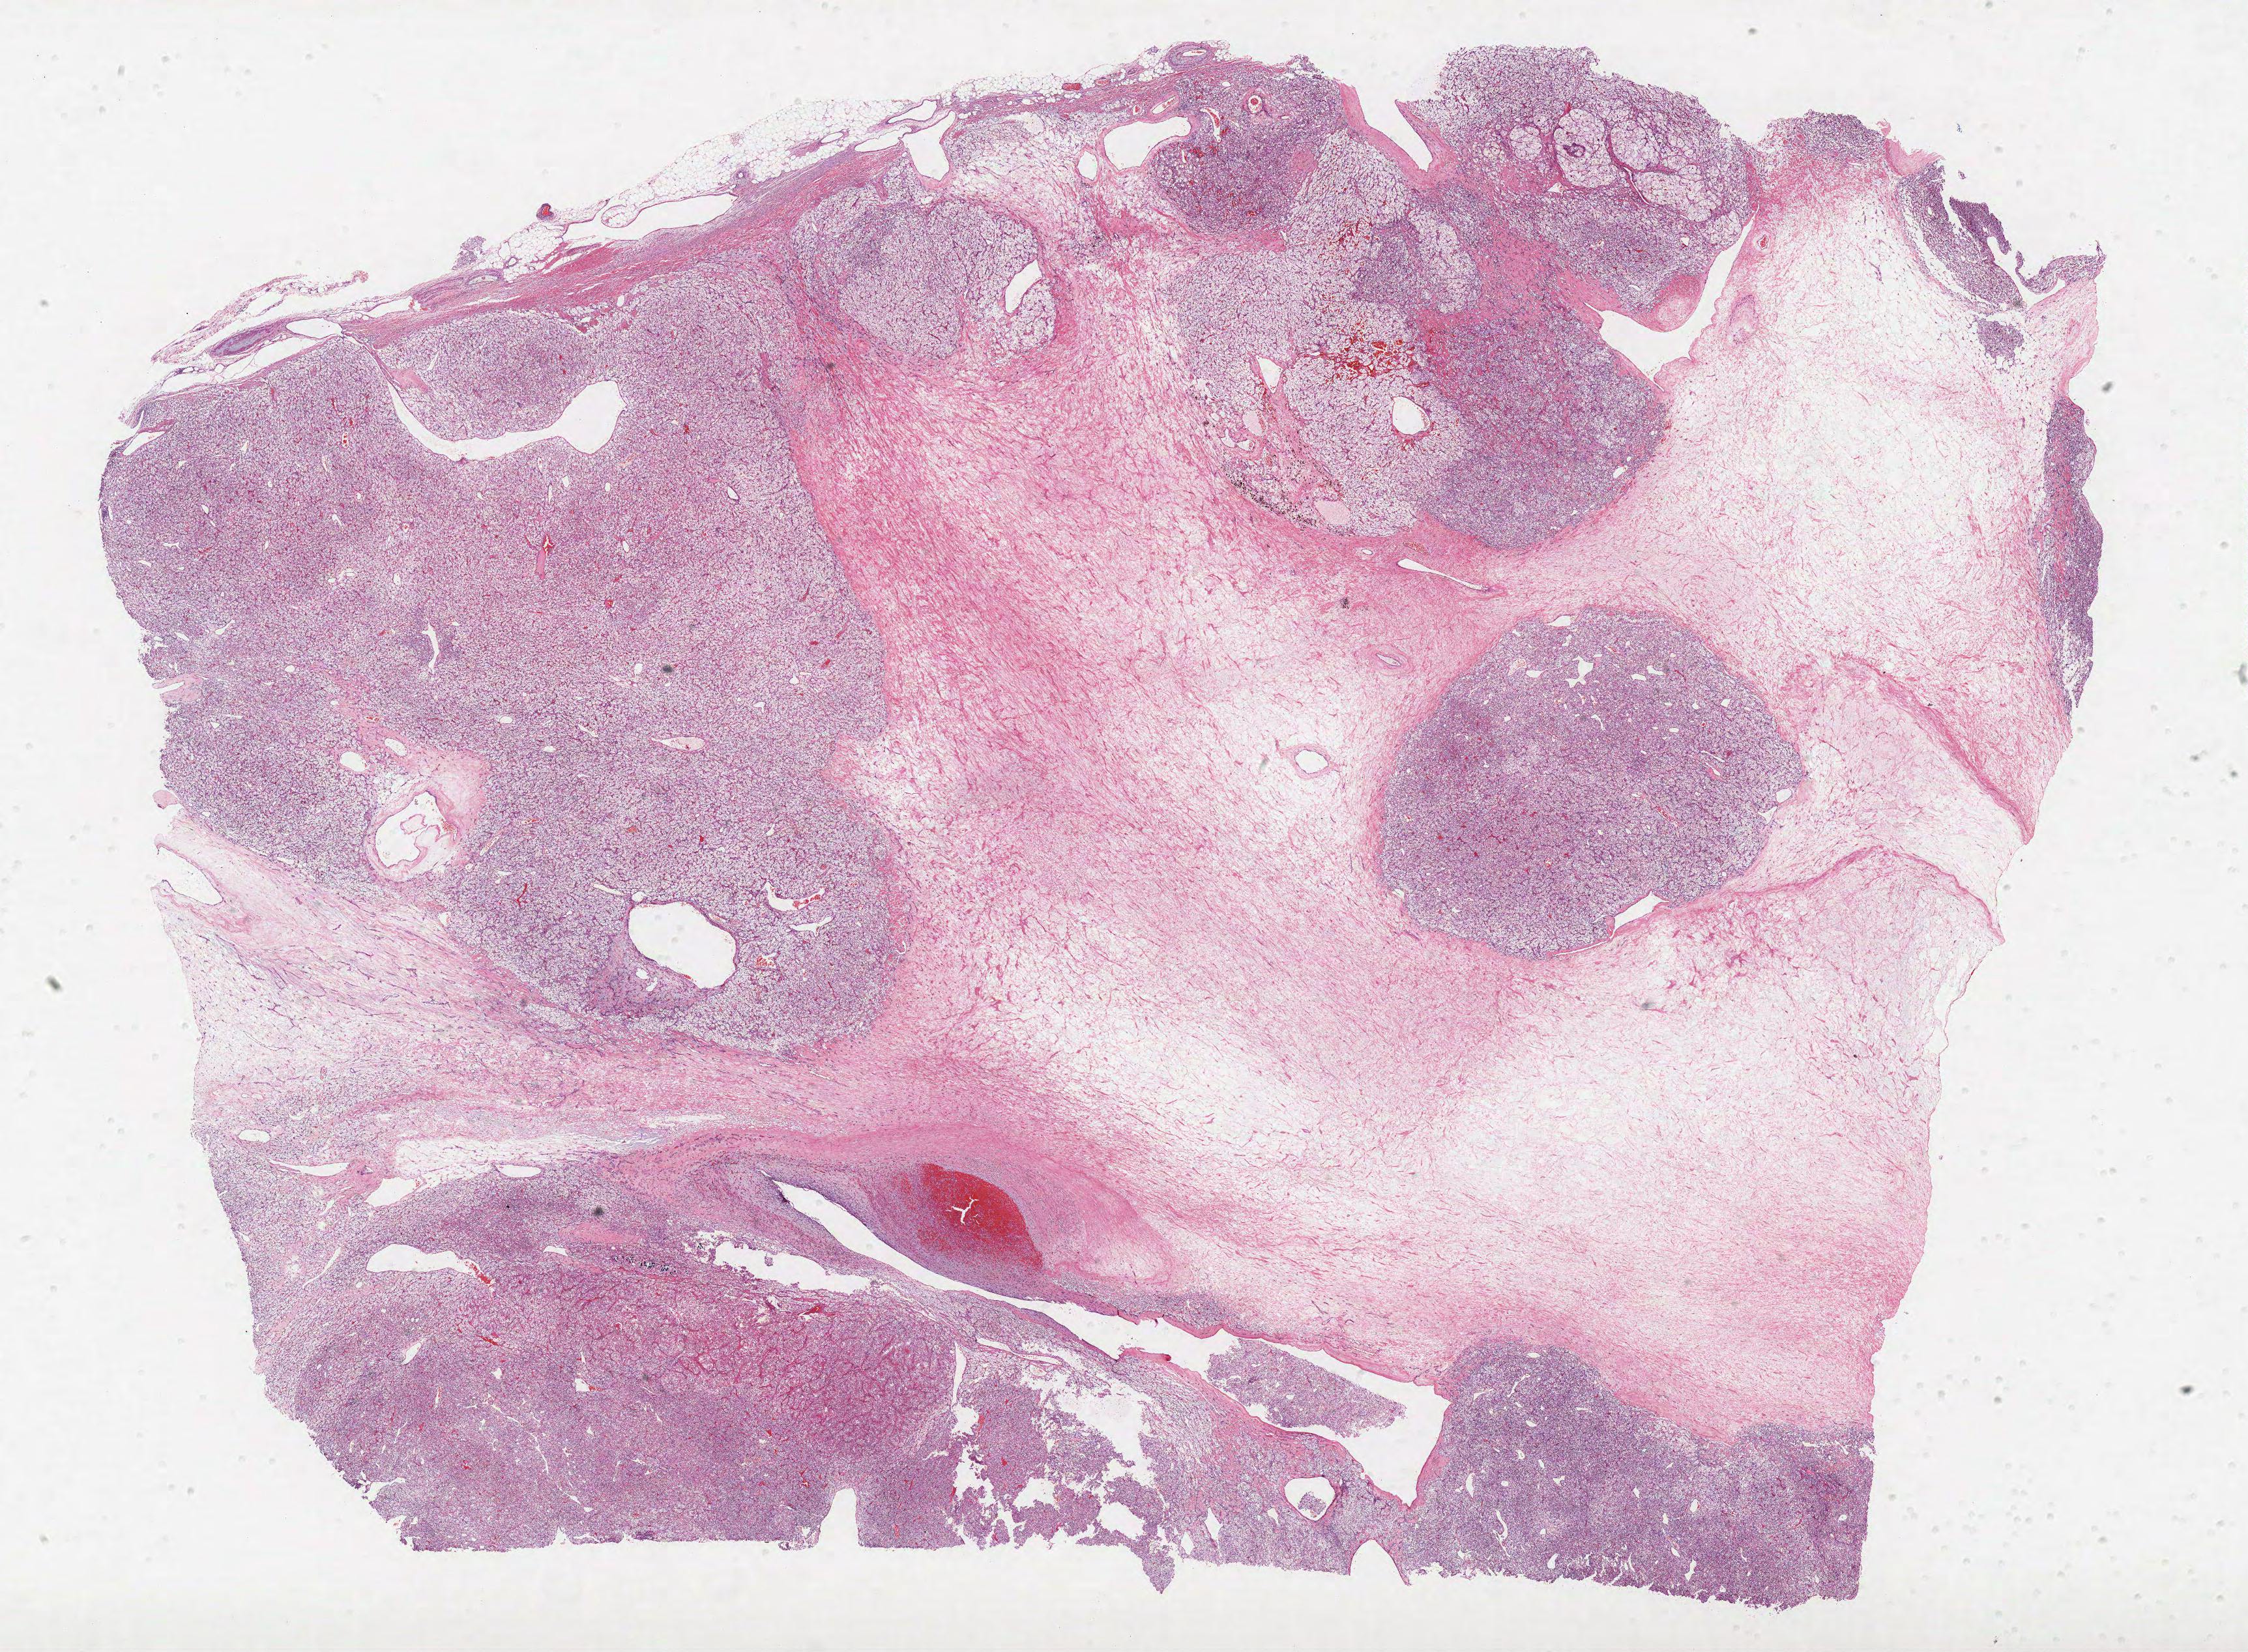
Digitized Hematoxylin and eosin (H&E) stained tissue section (whole slide), whole scanned area (about 27.6 x 20.3 mm, from a 40x scan) shown as a low-resolution overview, FFPE section, primary tumour sample from the kidney. Female patient; age at initial diagnosis 75 years. Histologic grade: G3 (poorly differentiated).
• histologic diagnosis: Clear cell adenocarcinoma, NOS
• AJCC pathologic stage: III
• TNM: T3a NX M0
• laterality: right